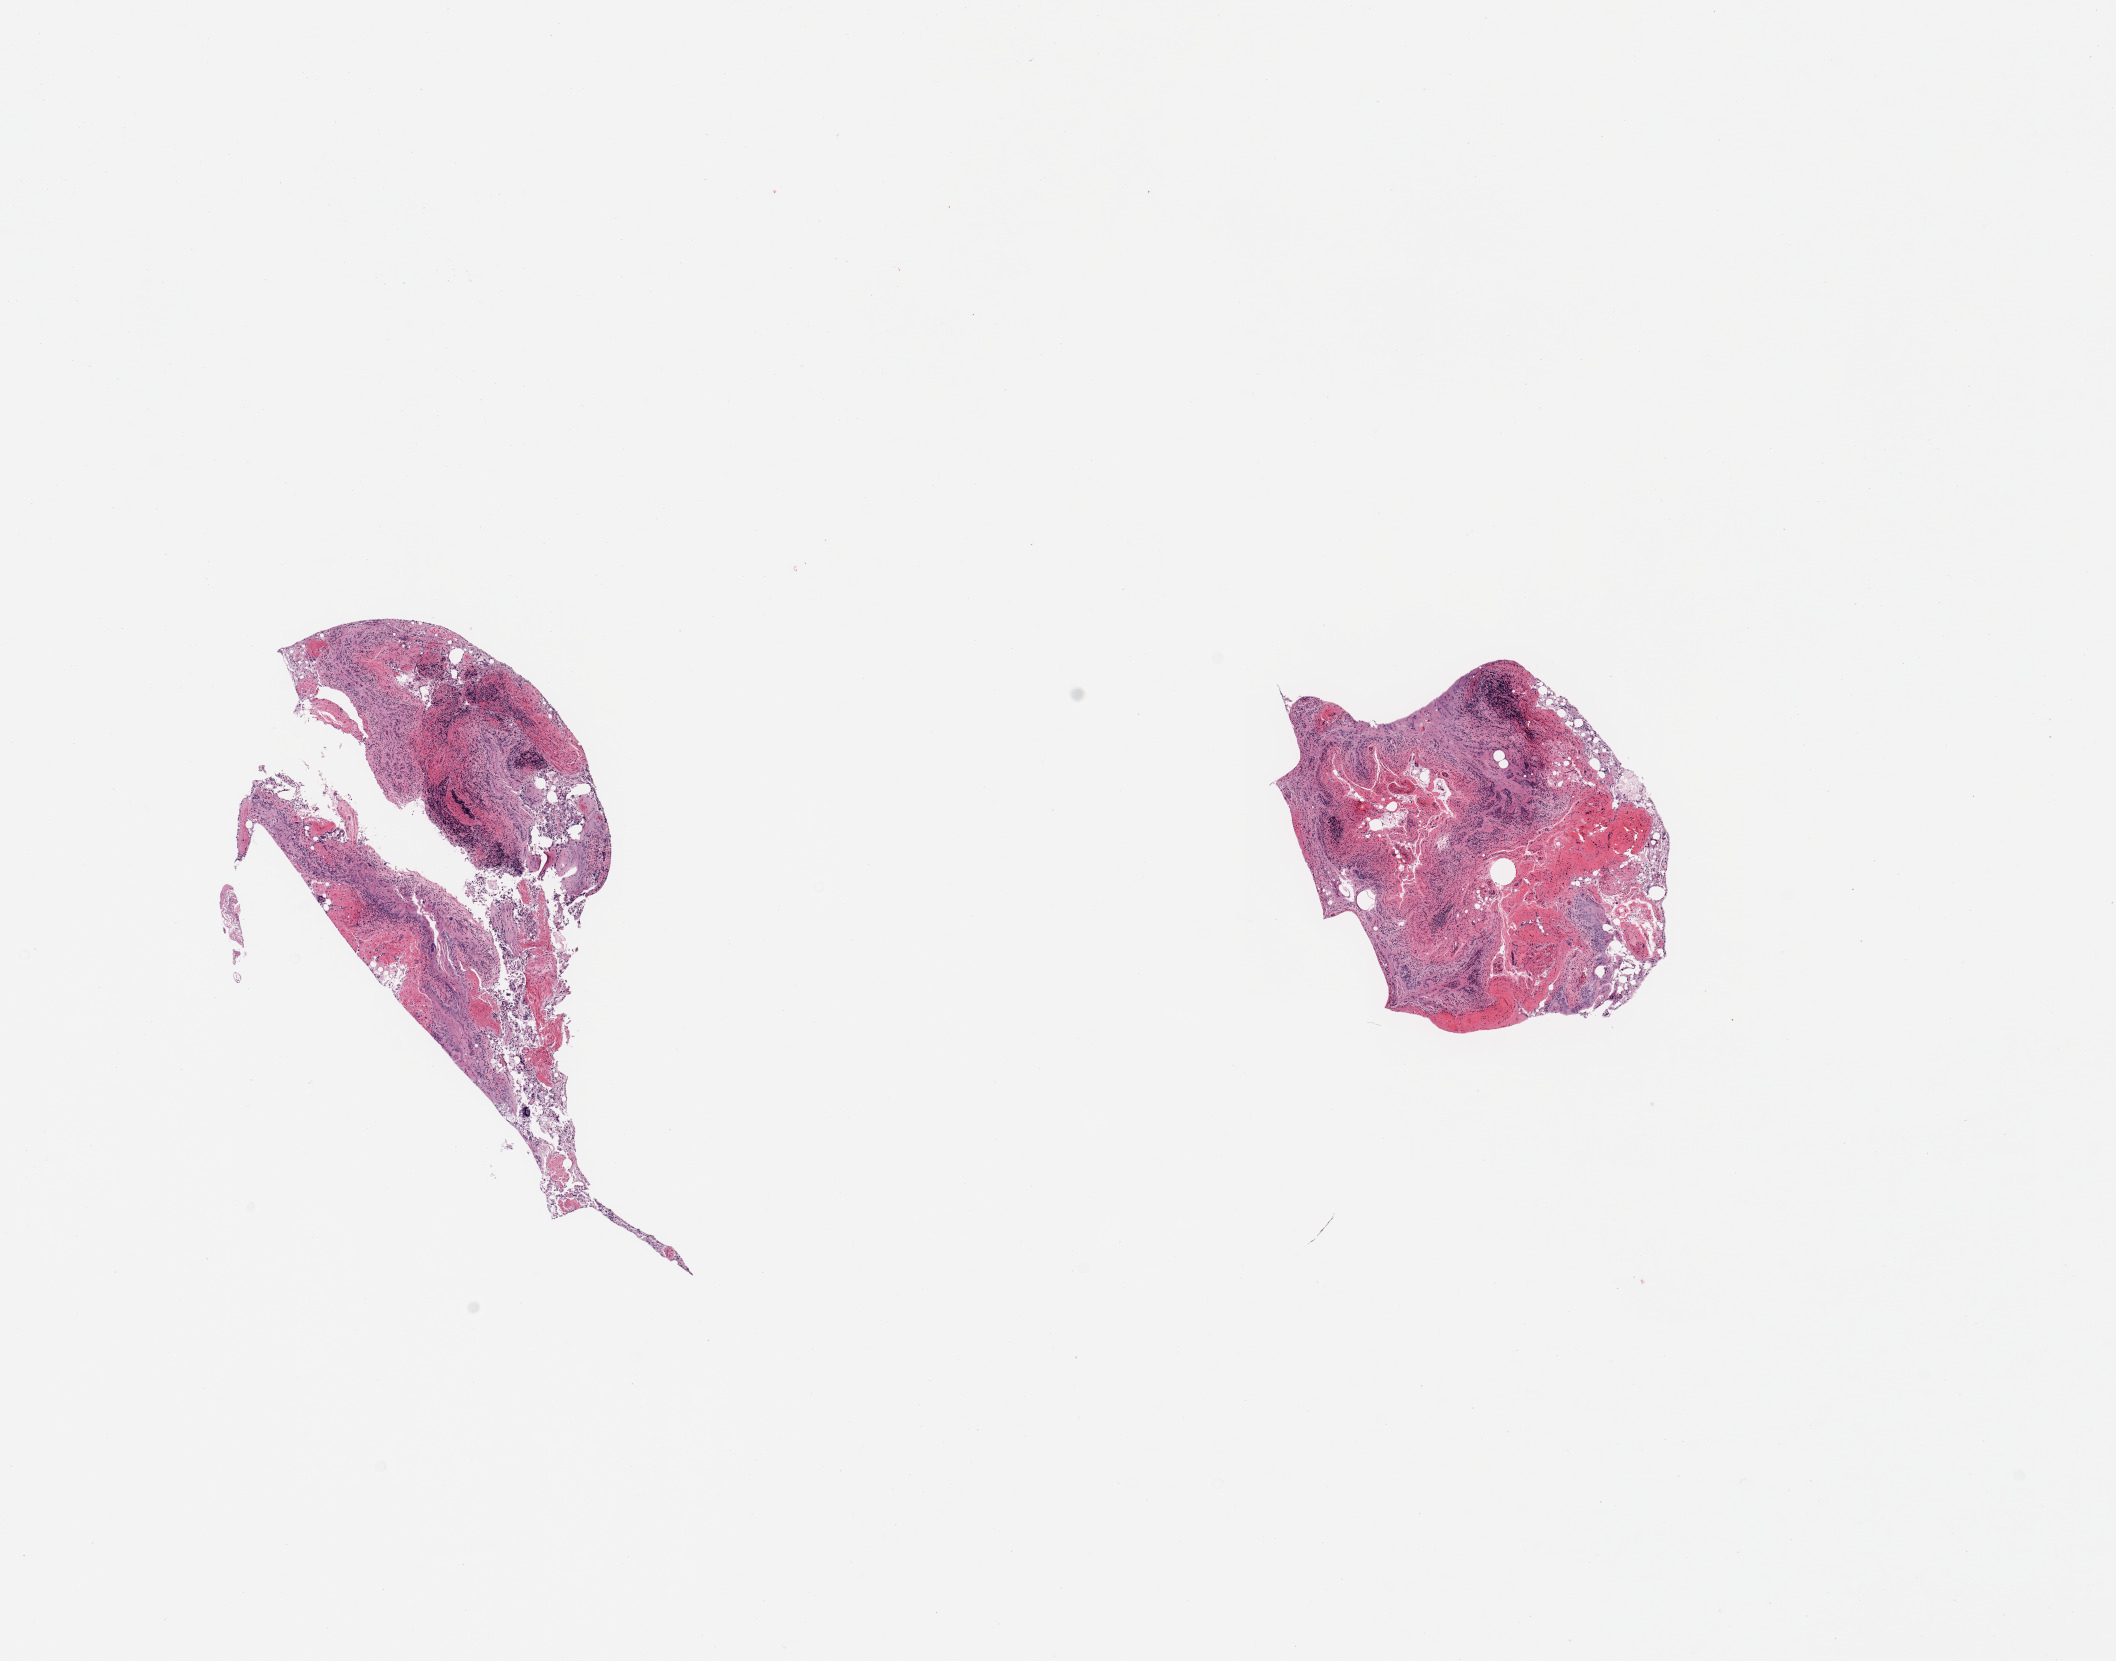
Whole-slide image, H&E stain, brightfield, shown as a low-resolution overview of the whole scanned area (about 16.7 x 13.1 mm, slide scanned at 20x); PAXgene-fixed, paraffin-embedded tissue; section of ileum (target tissue); donor tissue sample. Donor: male.
- reviewer comment on this tissue sample: 2 pieces; completely autolyzed mucosa with too little lymphoid tissue